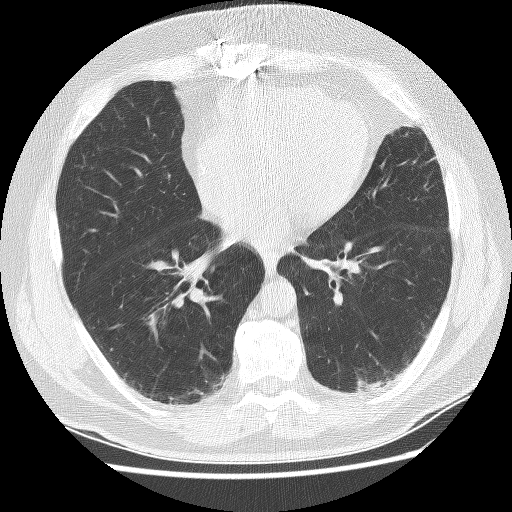
Low-dose screening chest CT, axial slice, baseline annual screen, lung window (W 1500 / L -600 HU), 2.5 mm slice thickness, lung (sharp) reconstruction kernel (BONE), slice 134 of 236 in the series, 512 × 512 image matrix. Male, age 65 years at enrolment. Former smoker at enrolment.
• Expert-annotated lung lesion, bounding box [x1, y1, x2, y2] px = [353, 371, 394, 406].
• No non-calcified nodule or mass ≥4 mm was recorded by the screening reader at this exam.
• Official screen result: negative screen, minor abnormalities not suspicious for lung cancer.
• Lung cancer was diagnosed 523 days after this screen (after the second annual screen): squamous cell carcinoma, NOS, left lower lobe, moderately differentiated (G2), stage IA (AJCC 6th edition), 20 mm at pathology.